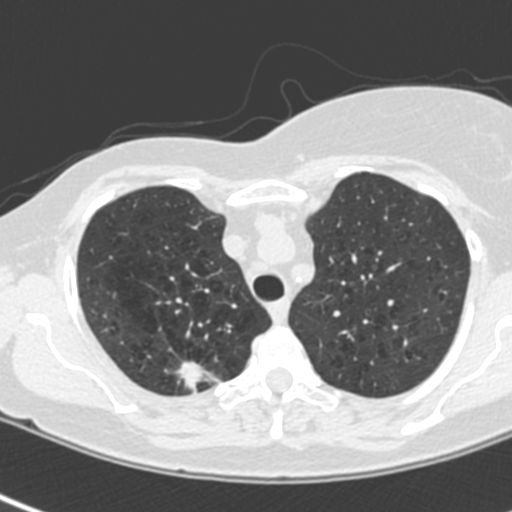
Low-dose screening chest CT, one axial slice; slice 176 of 214 in the series (ordered by position); lung window (W 1500 / L -600 HU); 1.3 mm slice thickness; 512 × 512 image matrix.
Outlined on this slice (manually delineated by an expert):
- lesion 1 (tumor, upper lobe of right lung): box from (x=177, y=361) to (x=206, y=392) px